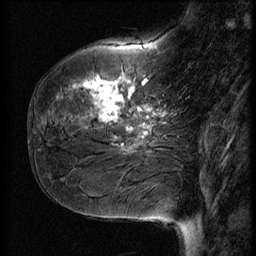
Breast MRI (dynamic contrast-enhanced), one sagittal slice. Position 19 of 56 along the scan axis. 3 images stored at this slice position (order not interpretable as contrast timing). 1.5 T. TE 4.2 ms, TR 9 ms. 2.5 mm slice thickness. 256 × 256 image matrix, field of view 180 × 180 mm. Female patient, age 51 years. From the clinical record (not read from this slice): setting: breast cancer imaged before/during neoadjuvant chemotherapy; receptor status: HR-positive, HER2-negative.
Annotated regions visible in this slice (semi-automatically segmented with operator editing):
- analysis volume of interest (the breast-tissue region the enhancement analysis was run in; not a lesion): bounding box [x1, y1, x2, y2] px = [41, 58, 167, 161]
- tumour enhancement mask (voxels above the 140 % enhancement threshold inside the analysis volume of interest): [73, 77, 158, 139]